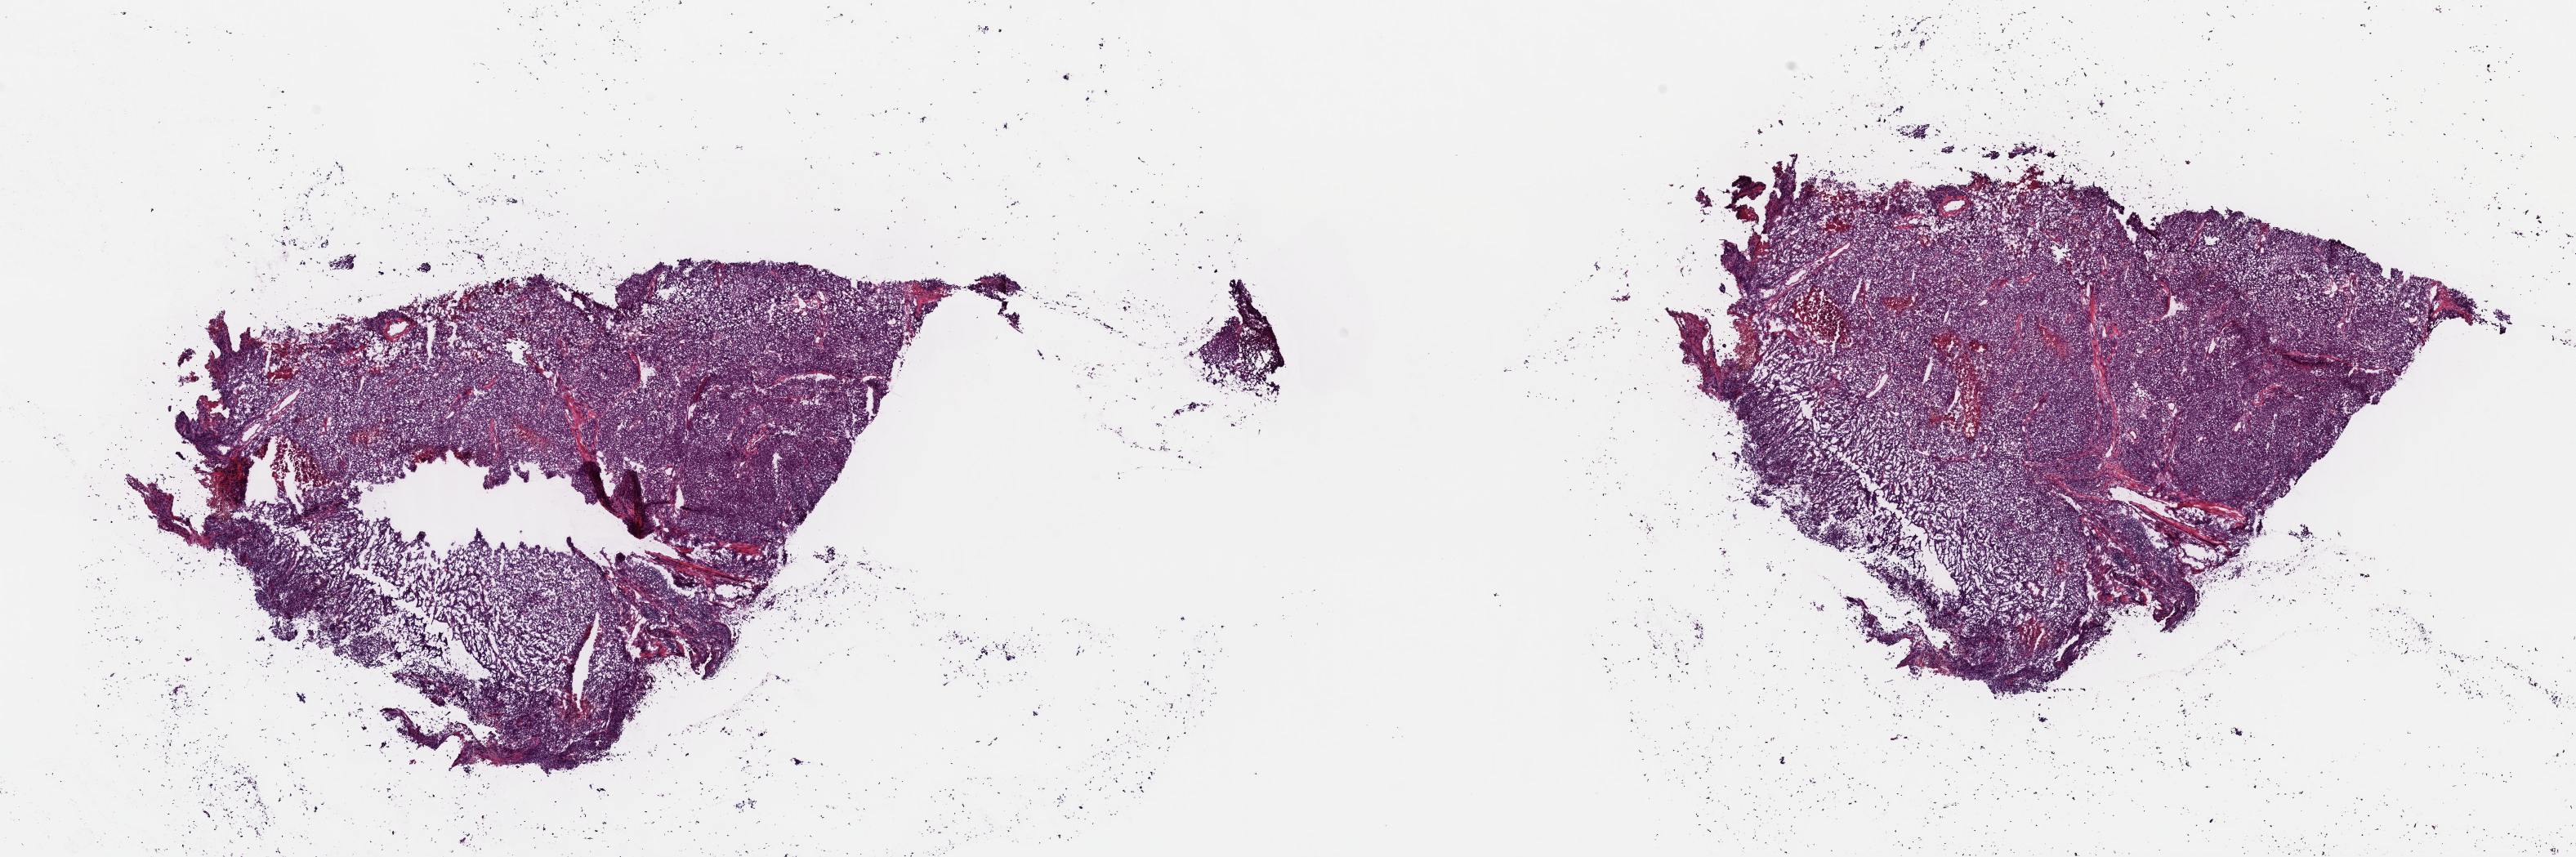
Hematoxylin and eosin (H&E) stained whole-slide image, shown as a low-resolution overview of the whole scanned area (about 24.9 x 8.3 mm), frozen section from the top of the tissue portion, metastatic tumour sample, sampled site: lymph nodes of axilla or arm. Male, age 39 years at initial diagnosis. Composition of this section per pathologist review: tumour cells 95%, tumour nuclei 95%, normal cells 0%, stromal cells 0%, necrosis 5%. Inflammatory infiltration, as recorded: lymphocyte infiltration 0%, monocyte infiltration 0%, neutrophil infiltration 0%.
- this section: metastatic tumour tissue
- patient diagnosis: Malignant melanoma, NOS